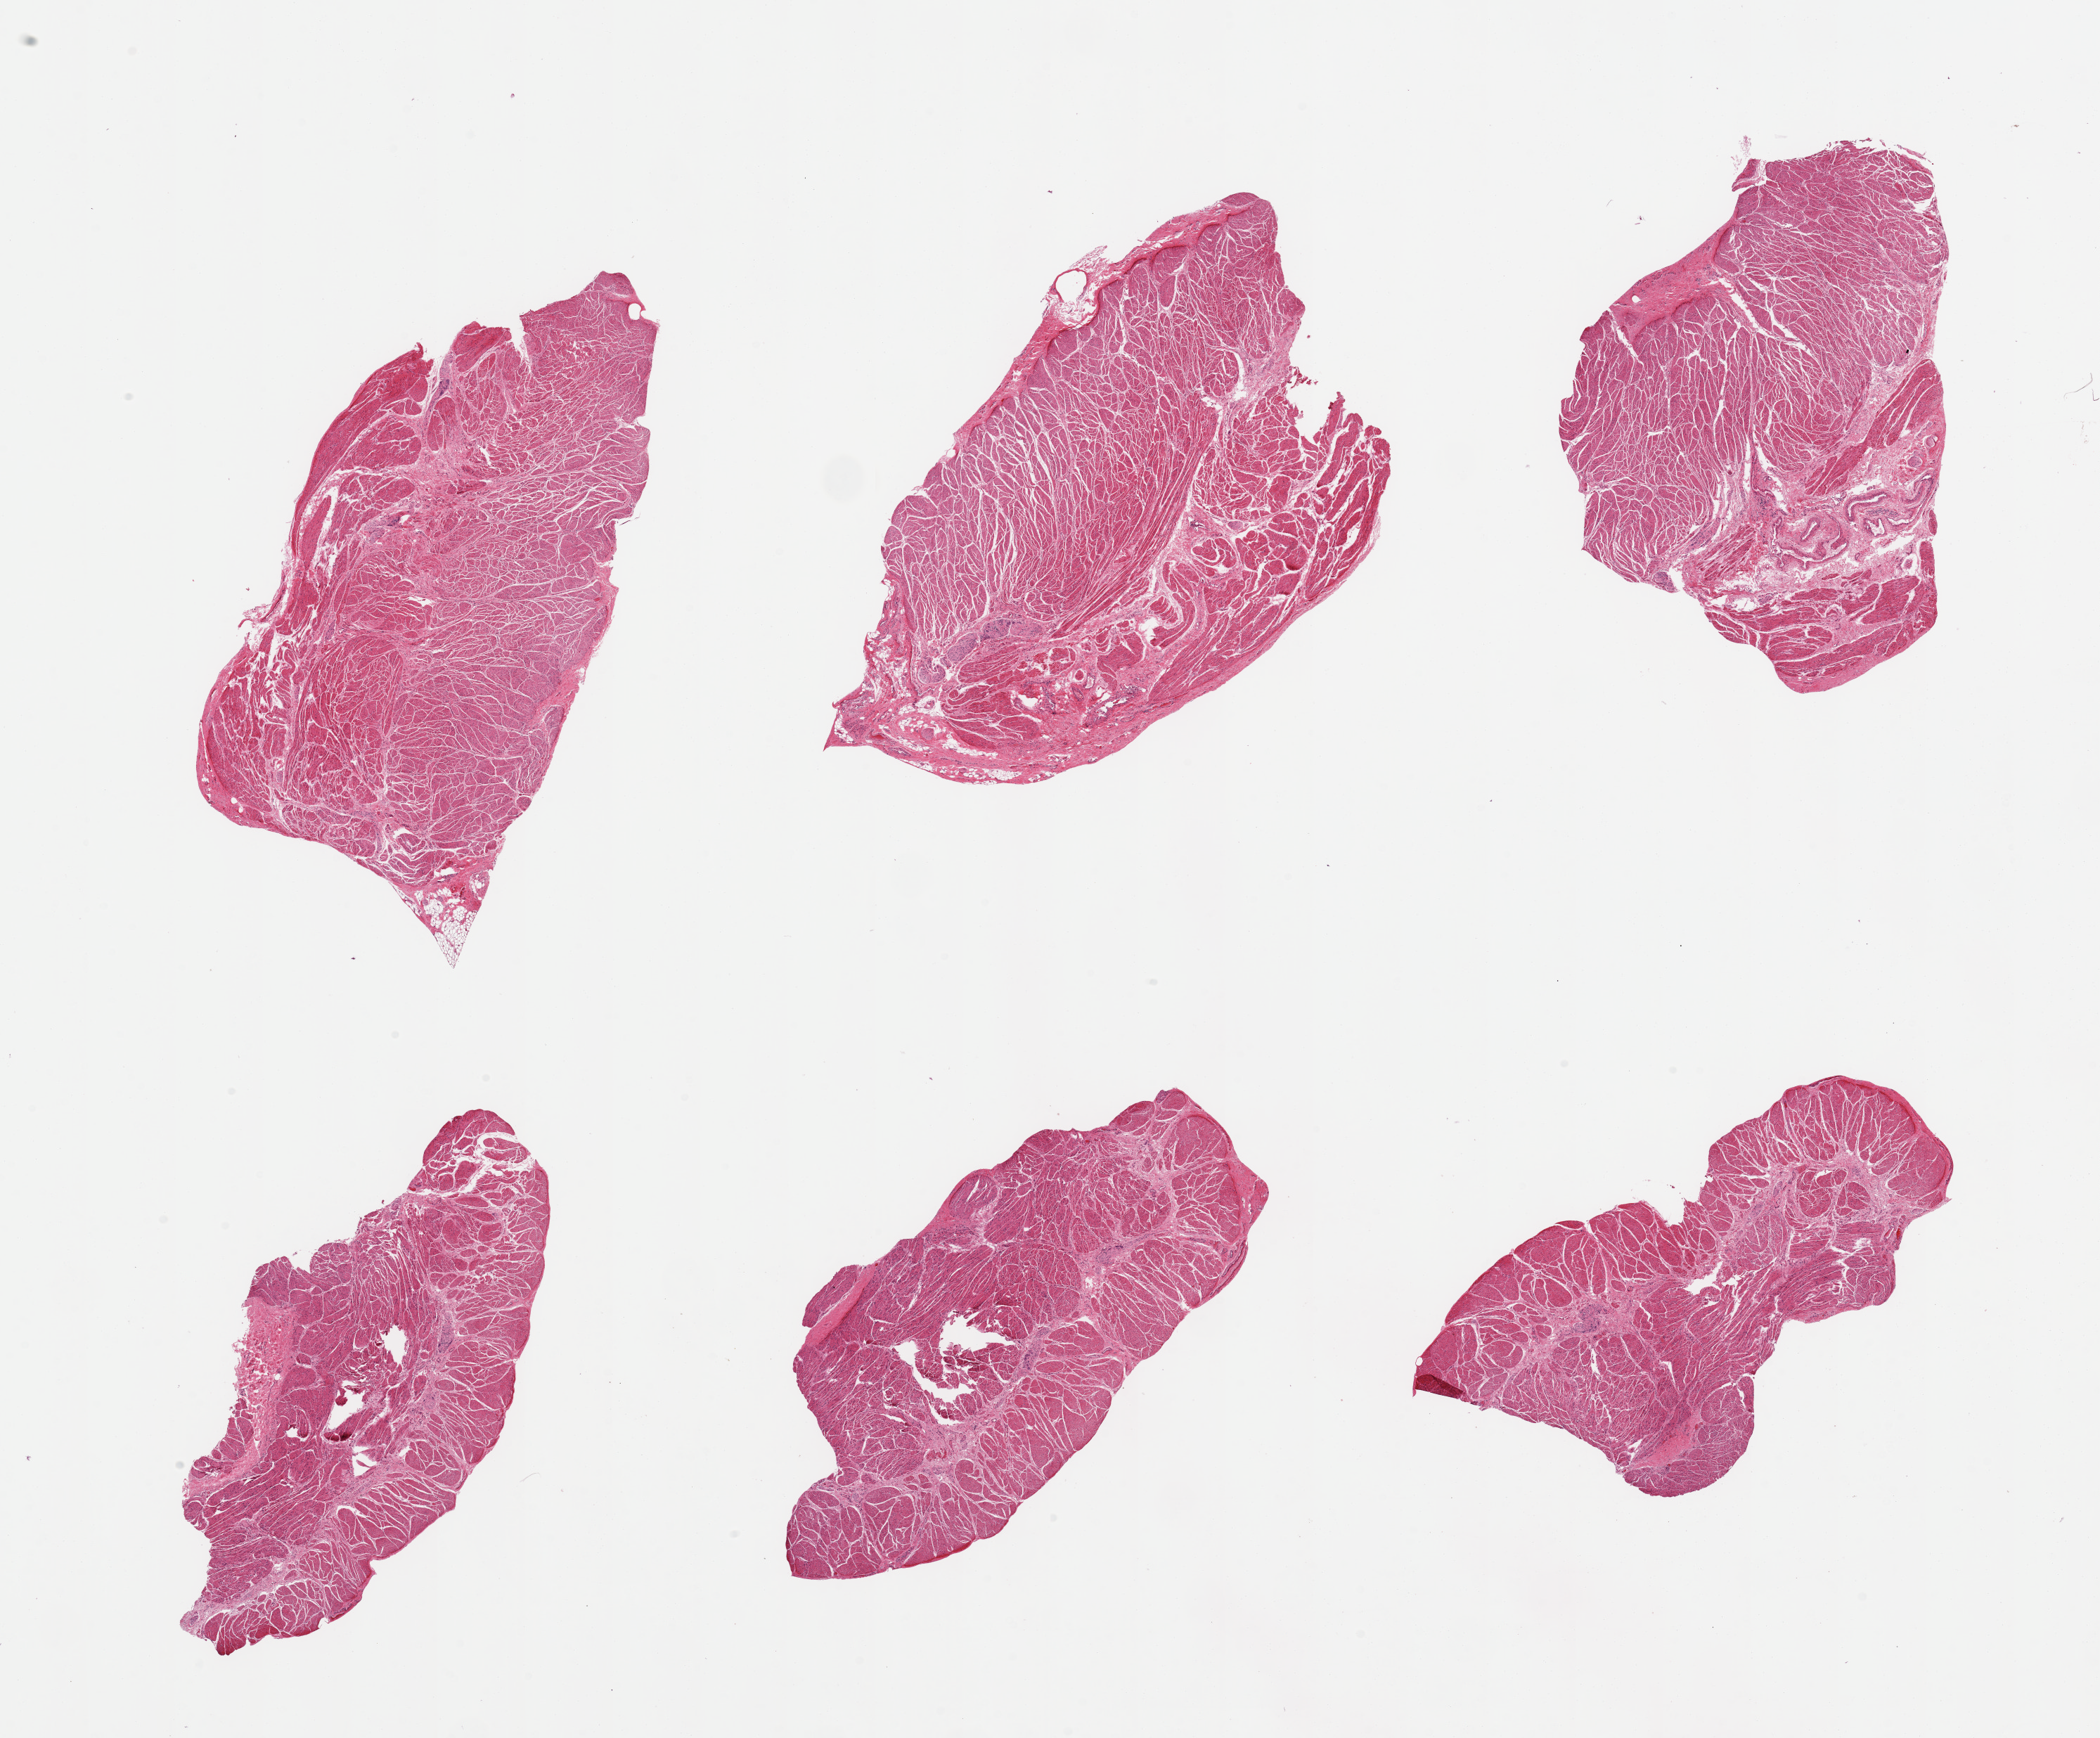
H&E whole-slide image, brightfield, low-resolution overview of the scanned area, about 23.6 x 19.6 mm; PAXgene-fixed paraffin-embedded (PFPE) section; sampled site (target tissue): gastroesophageal junction; tissue donor sample. Donor: male.
• review note (as recorded): 6 pieces, confirmed target muscularis